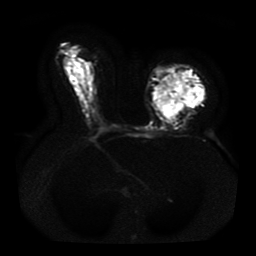
Breast MRI, one axial slice; position 23 of 41 along the scan axis; diffusion-weighted series; image 2 of 4 stored at this slice position (different b-values; order by instance number); 1.5 T; 256 × 256 image matrix, field of view 330 × 330 mm. Female patient.
Structures marked on this image (expert manual segmentation):
- tumour on diffusion-weighted imaging: bounding box (x1, y1, x2, y2) in pixels: (154, 72, 204, 117)